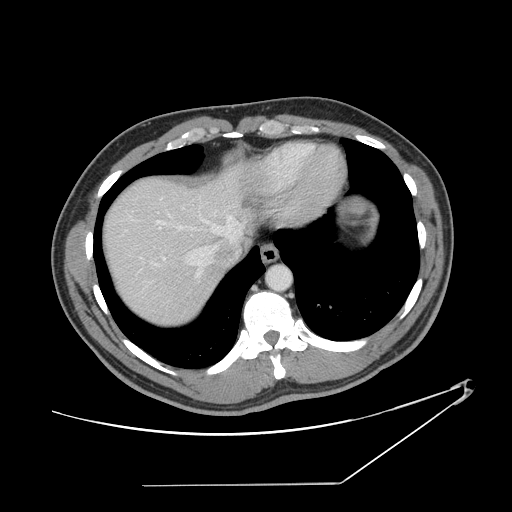
Contrast-enhanced abdominal CT, one axial slice. Slice 127 of 152 in the series (ordered by position). 120 kVp. Intravenous contrast given. Soft-tissue window (W 400 / L 40 HU). 512 × 512 image matrix. Male patient, age 45 years. Case-level facts recorded for this patient, not image findings: diagnosis: colorectal cancer liver metastases, imaged before liver resection; multiple liver metastases: no; largest metastasis: 1 cm; disease in both lobes: no.
Annotated regions visible in this slice (manually delineated by an expert):
- hepatic veins: box from (x=125, y=198) to (x=240, y=278) px
- liver: (x=106, y=172)–(x=251, y=323)
- planned liver remnant (the part of the liver to remain after resection): (x=106, y=179)–(x=231, y=323)
- liver metastasis: (x=242, y=198)–(x=252, y=209)